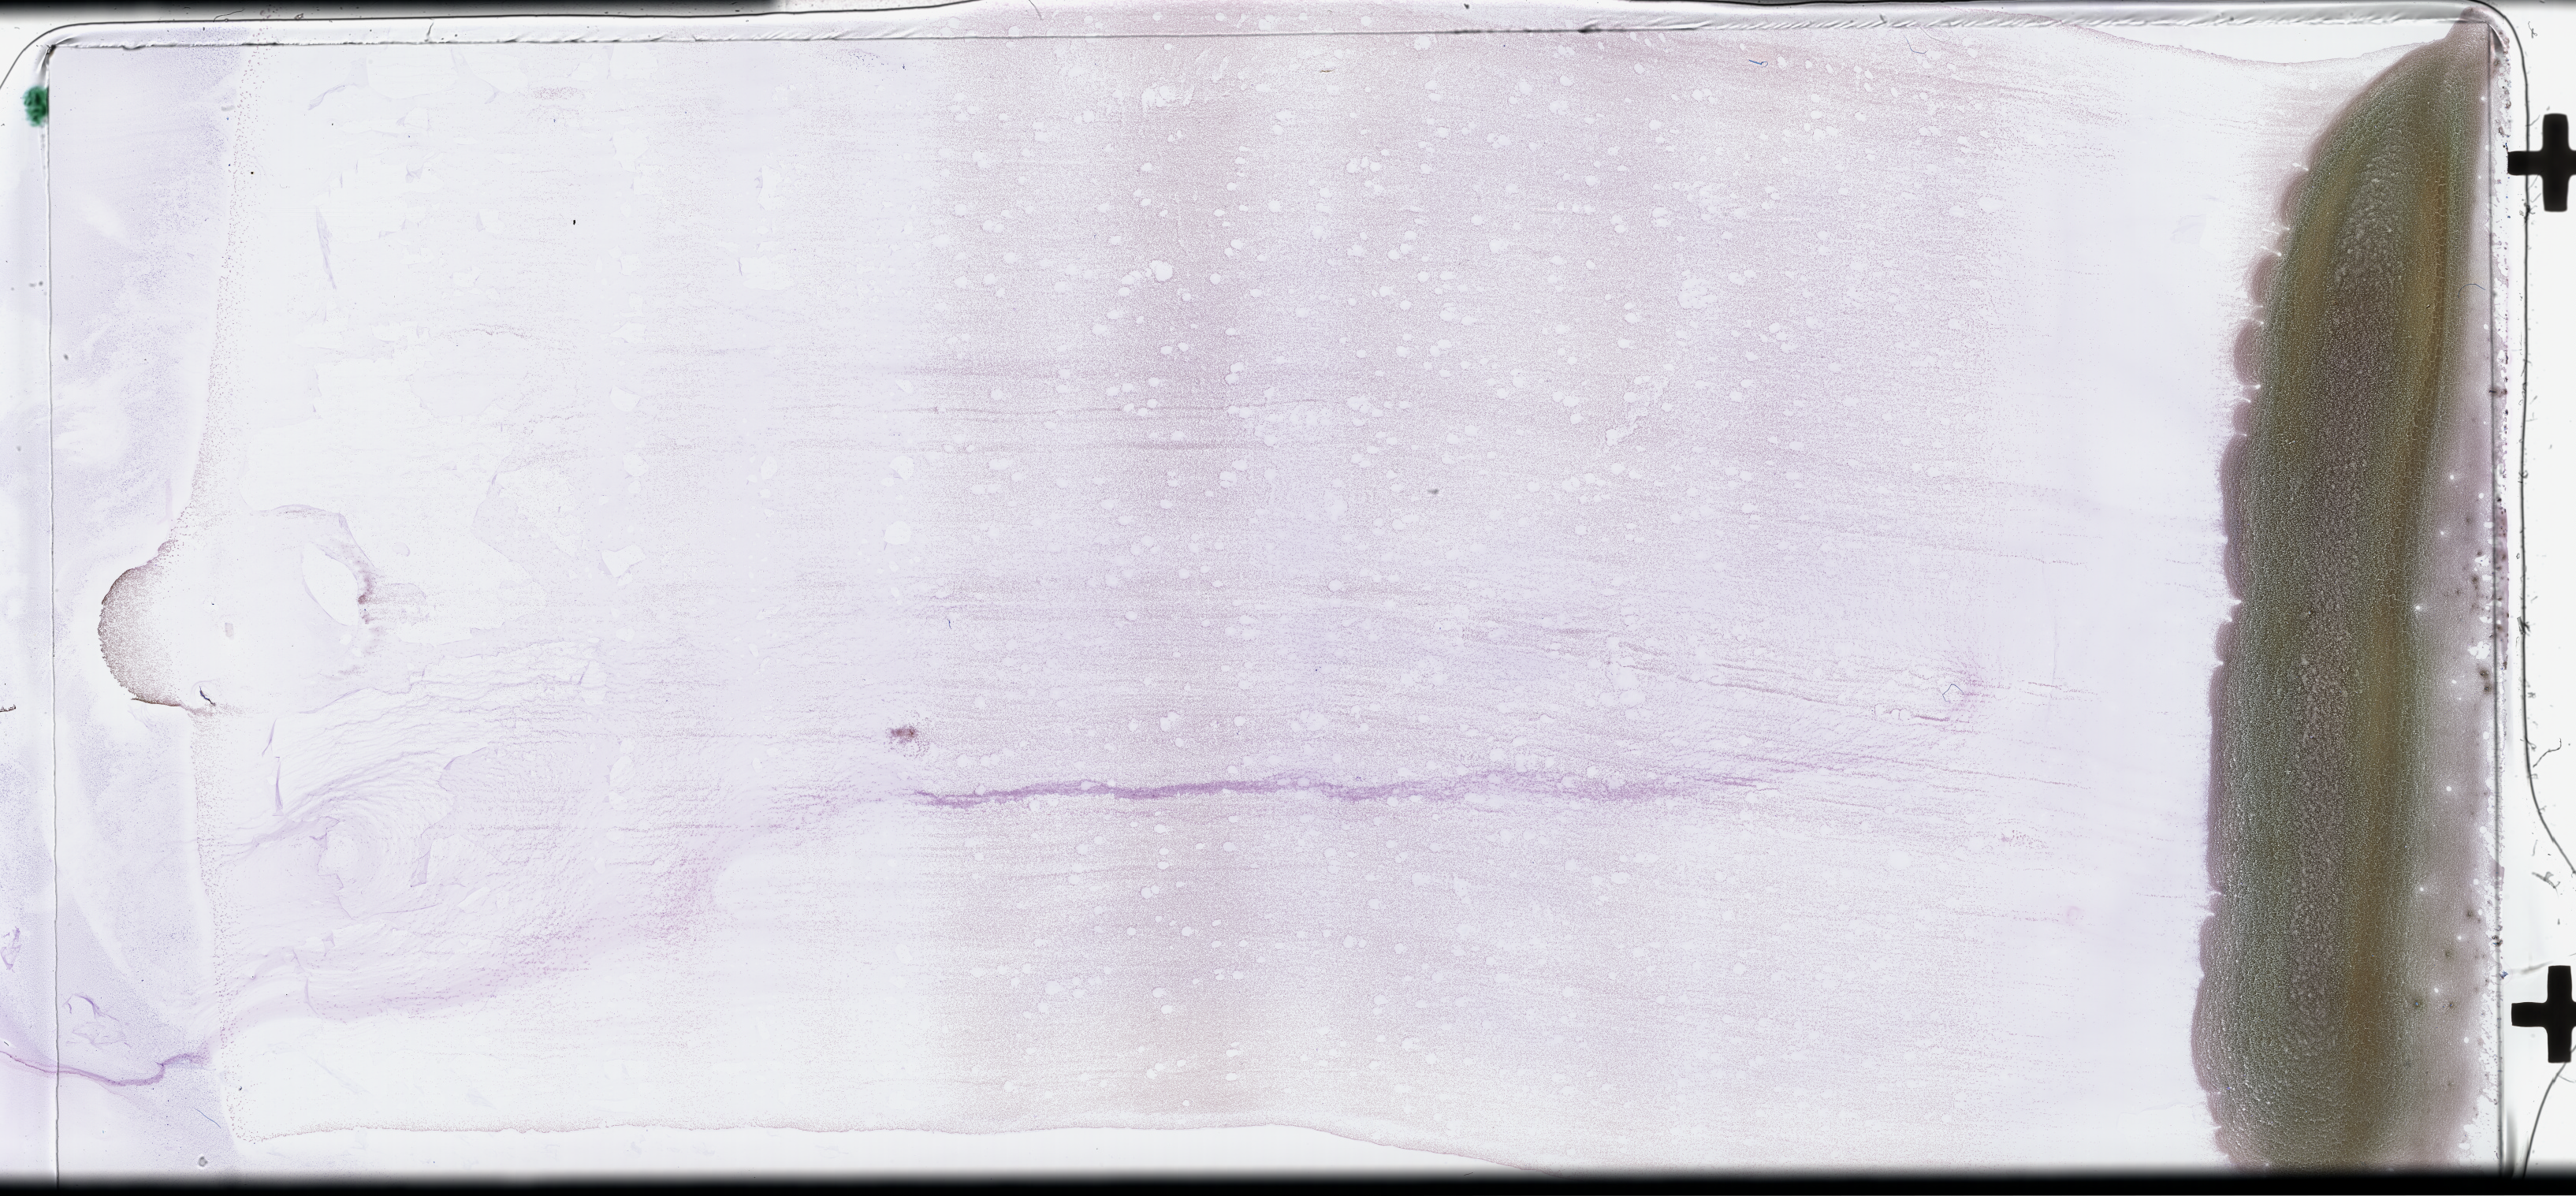
Whole-slide image of a whole blood smear, Wright-Giemsa stain, a low-resolution overview of the entire scanned area, about 52.8 x 24.5 mm, collected at baseline (before treatment). Patient sex: female.
Patient diagnosis: Plasma Cell Myeloma.